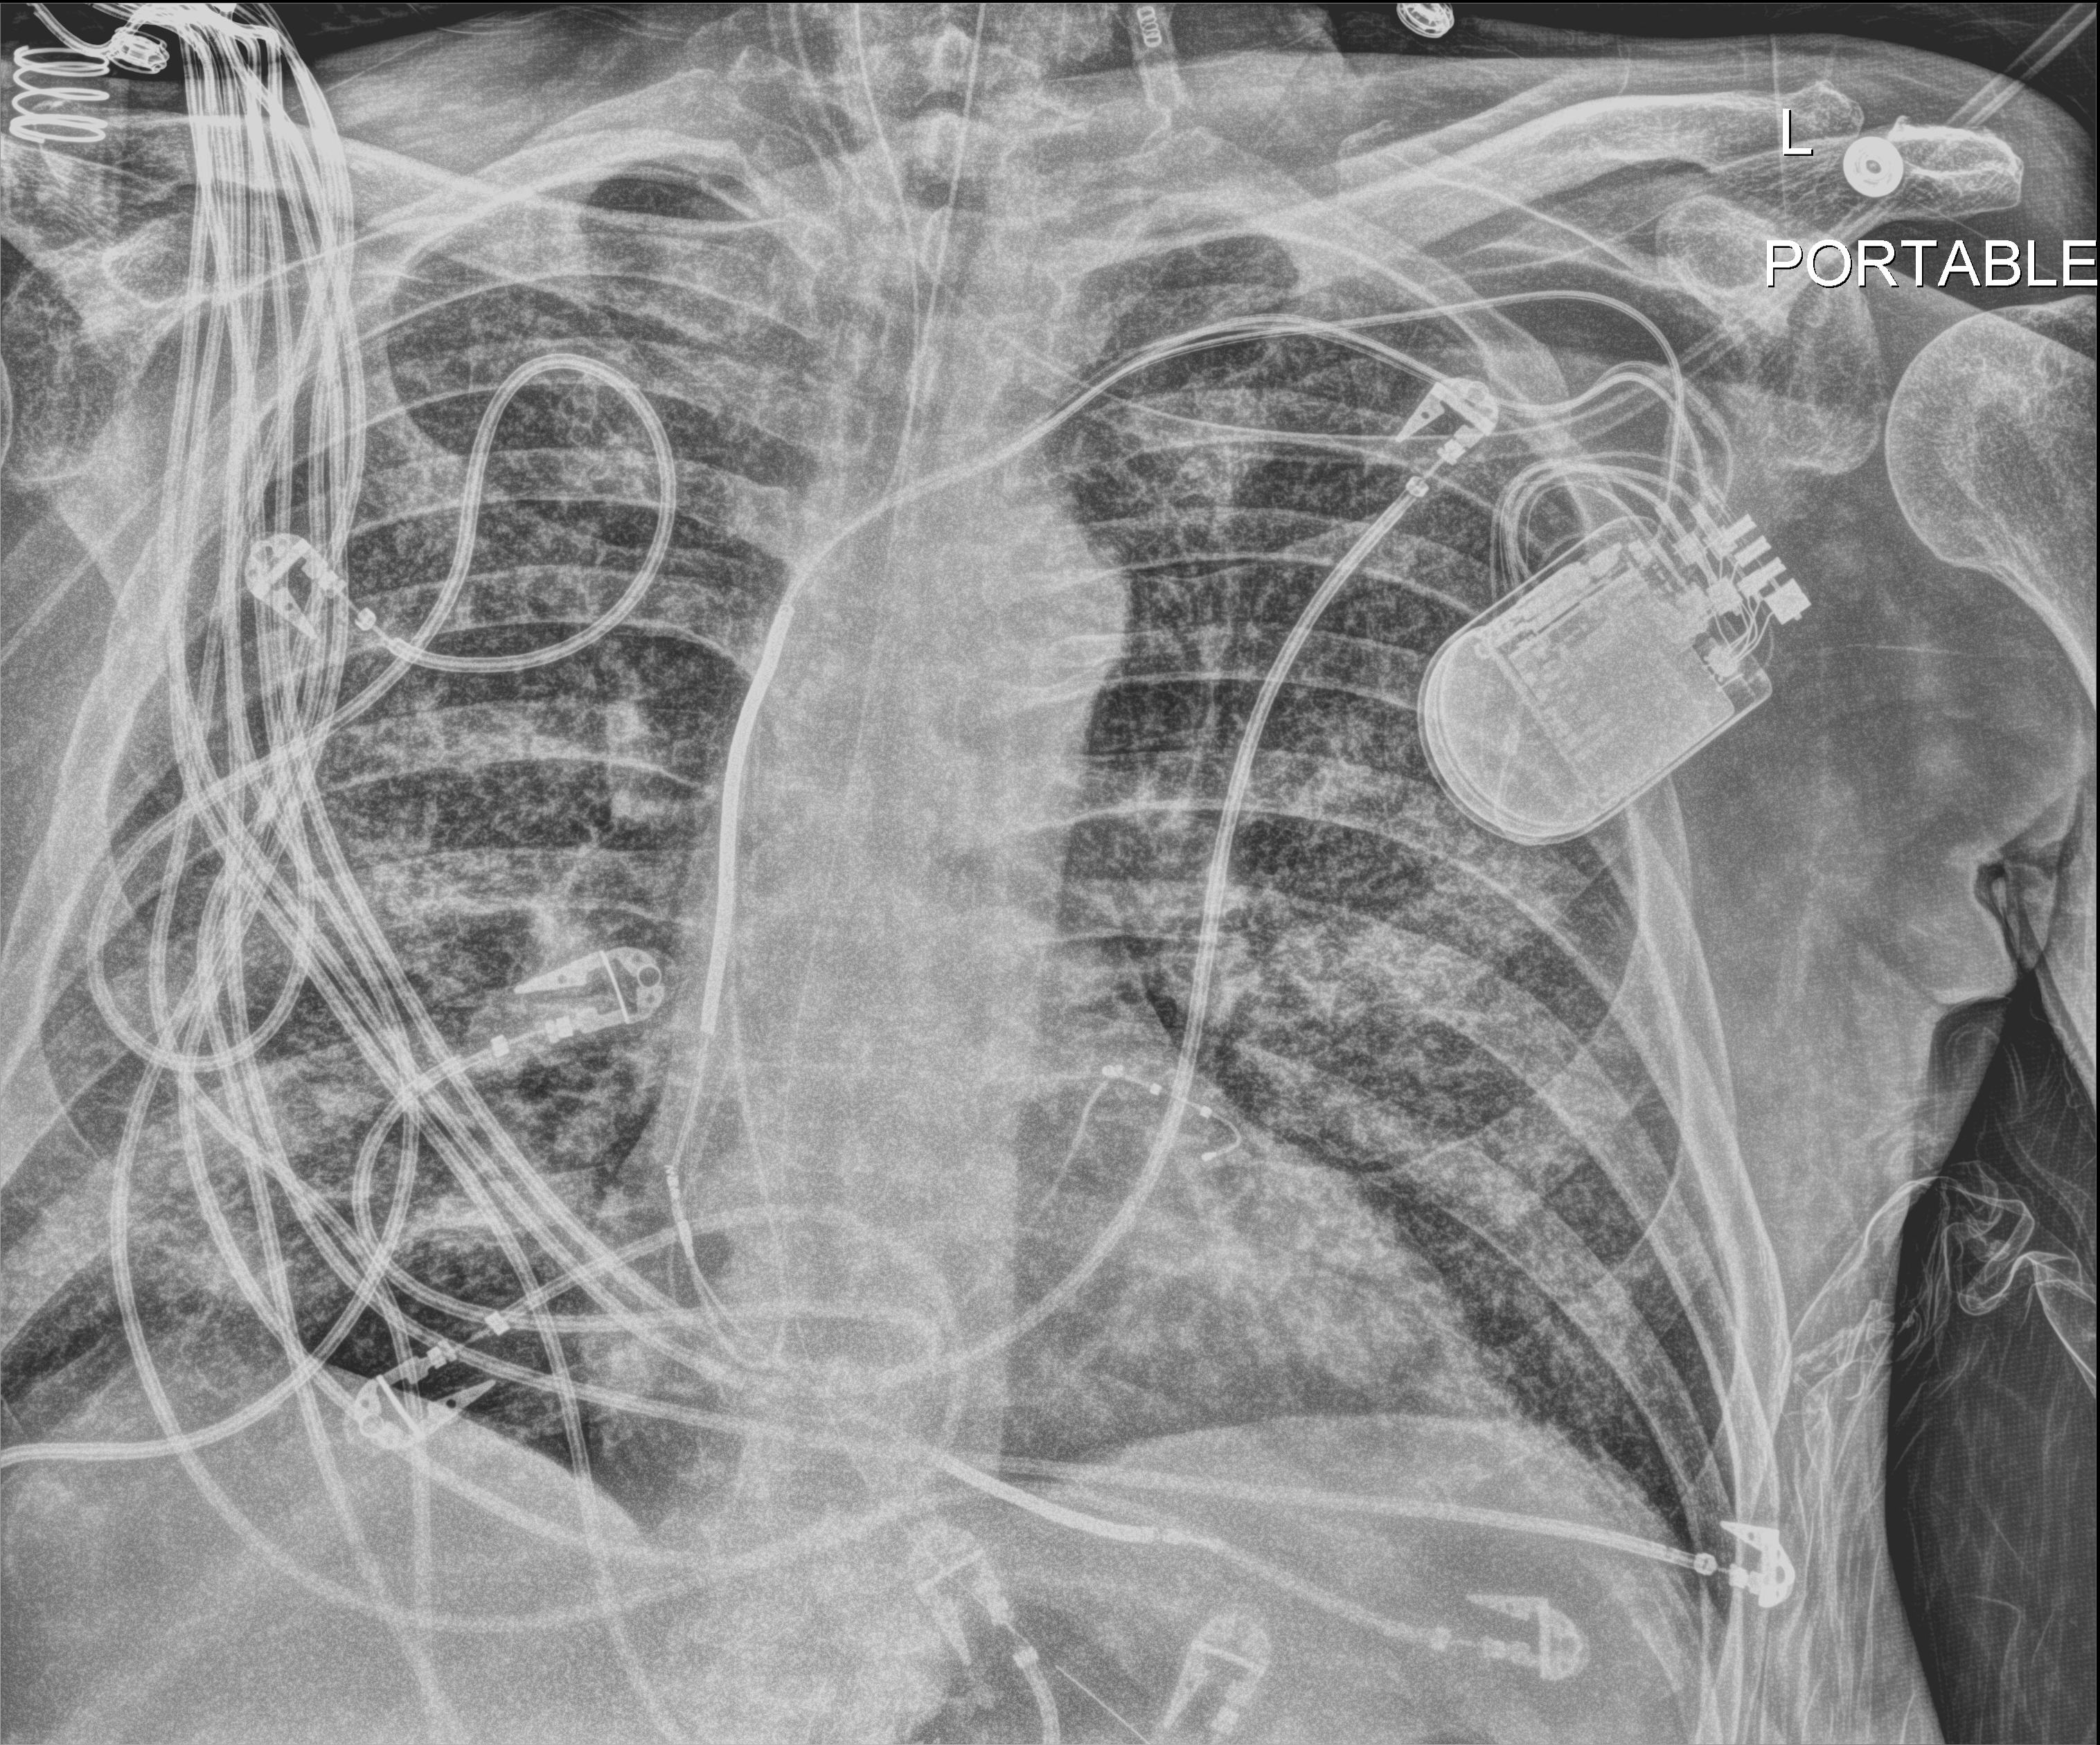
Bedside chest radiograph (digital radiography), anteroposterior (AP) projection. Patient hospitalised with COVID-19; male, aged 60–74 years.
Hospital-stay facts (about this admission, not read from this image; timing relative to this image not recorded):
- smoking status (admission record): former
- chronic kidney disease (admission record): no
- admitted to intensive care during this hospital stay: yes